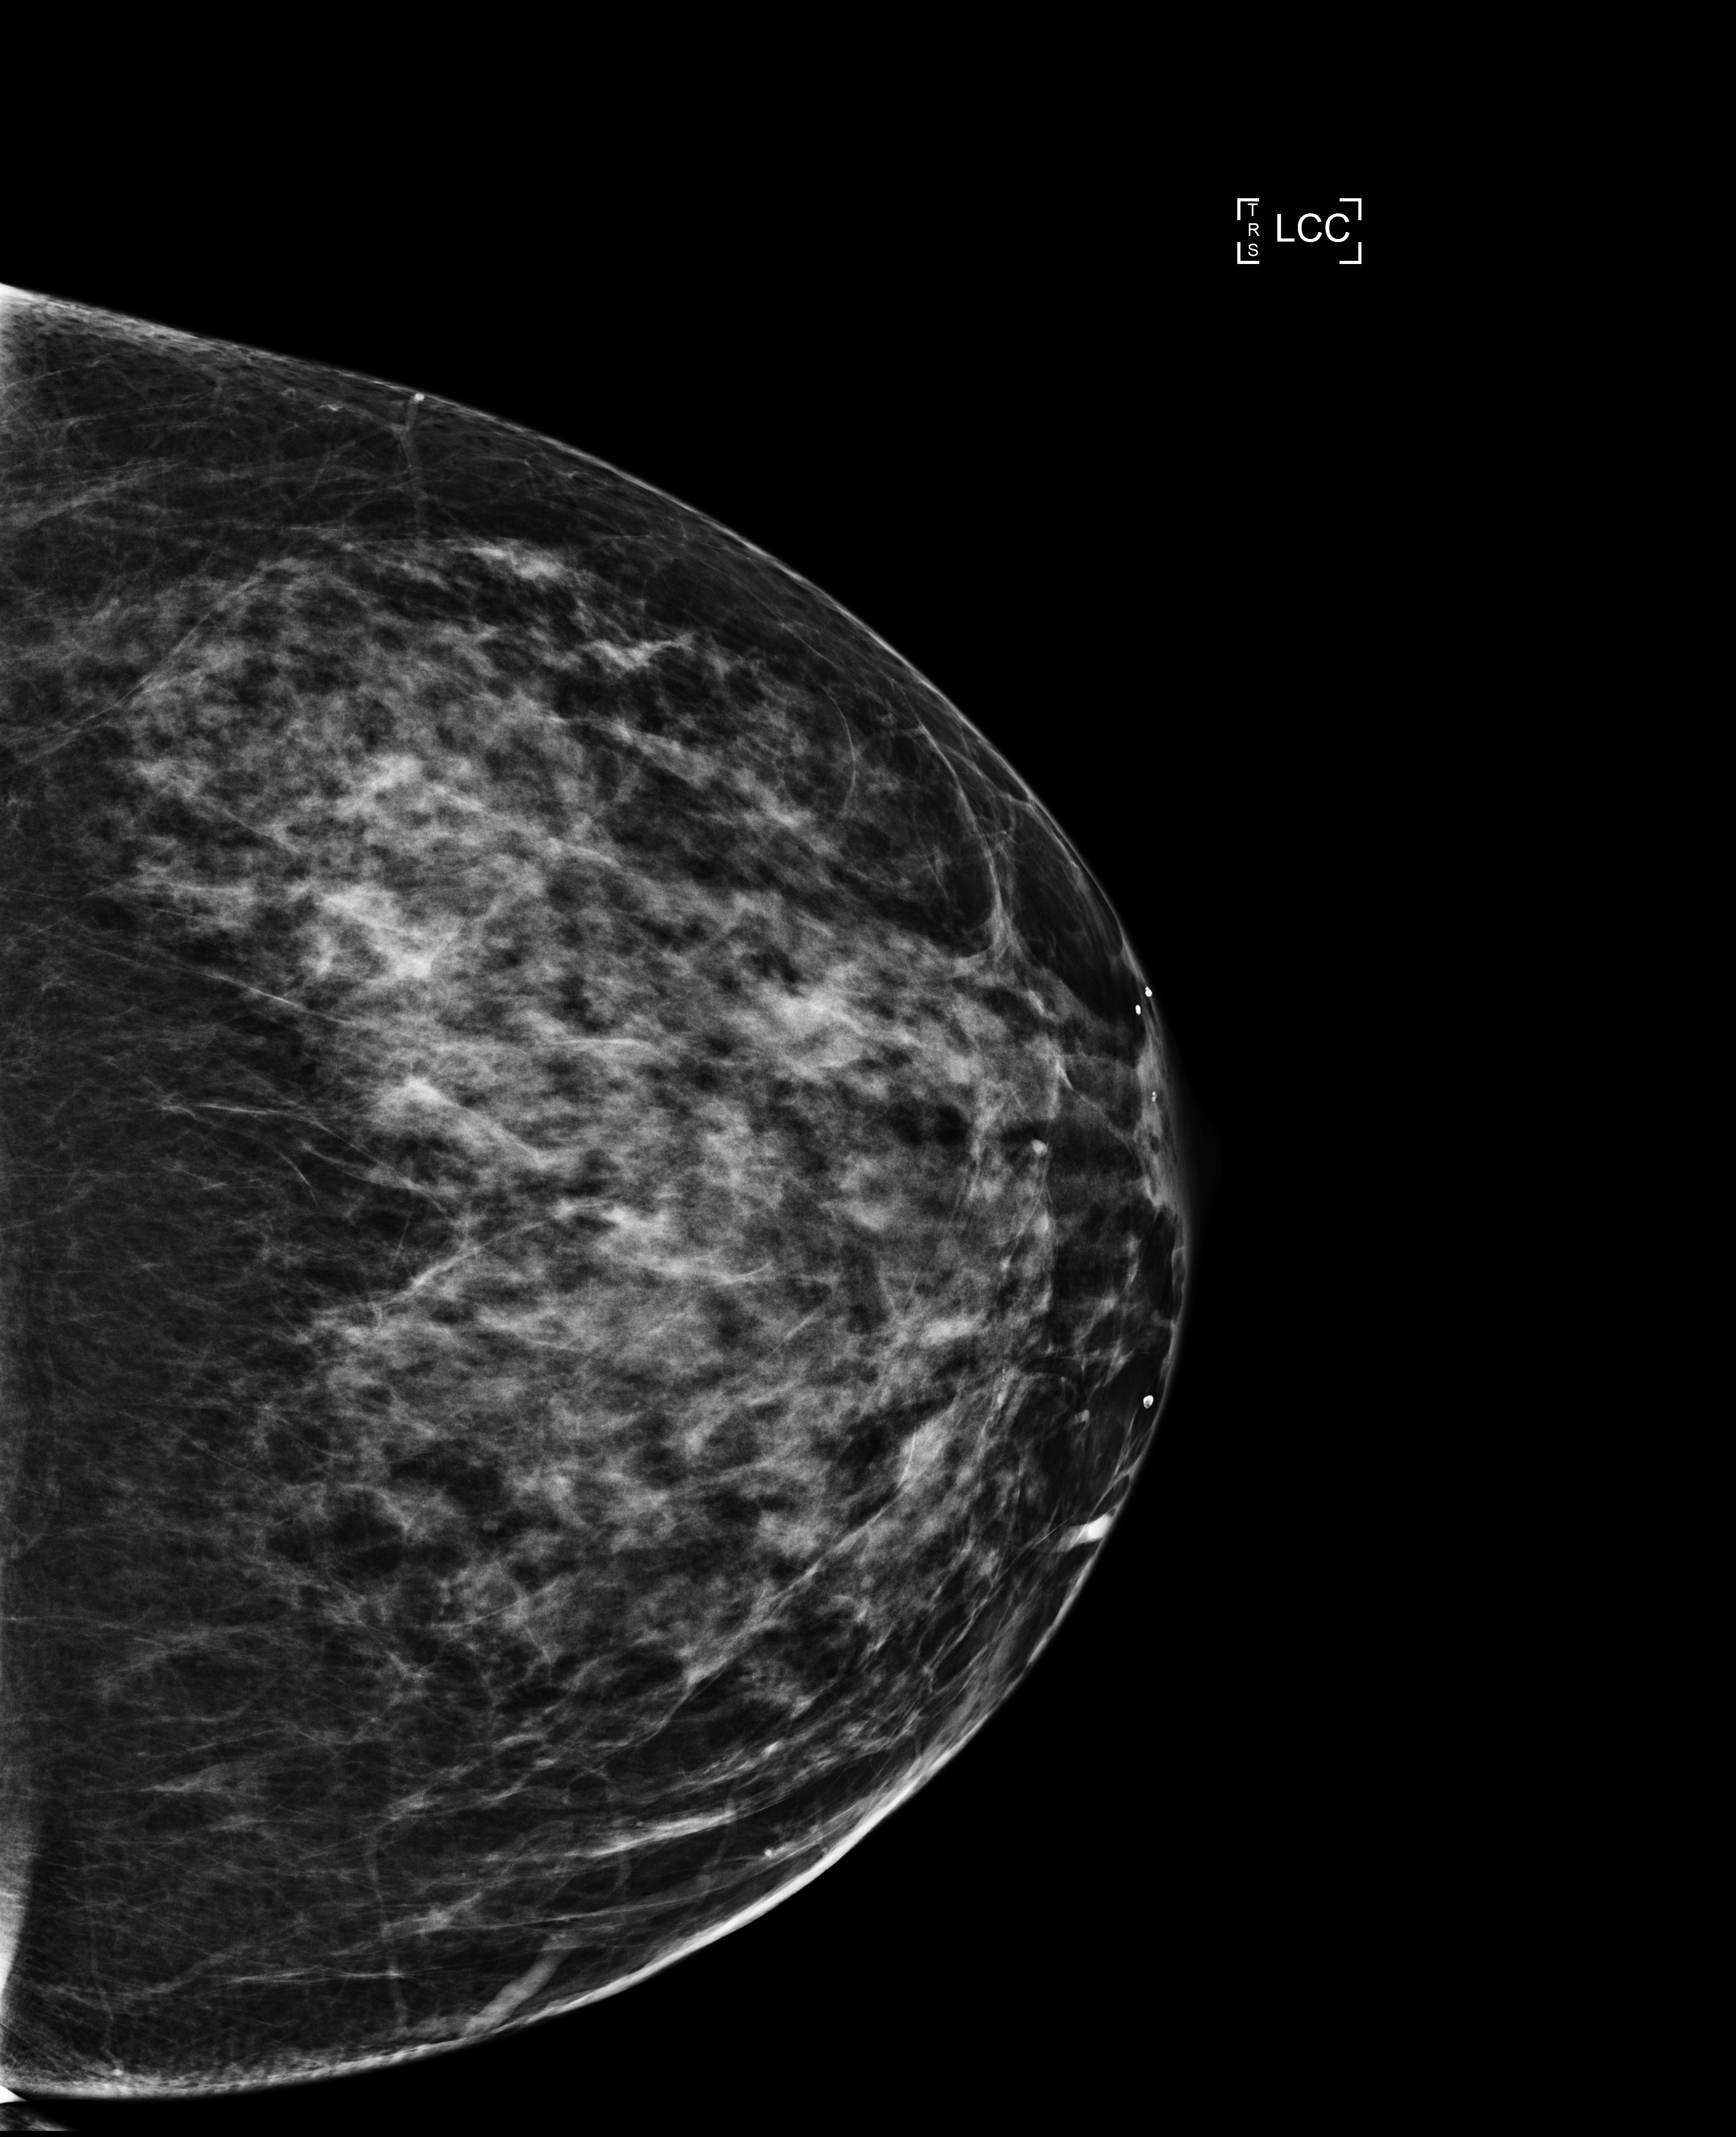
Annual screening mammography examination; compressed breast thickness 76 mm. Patient aged 45 years (female).
Image type: full-field digital mammogram. Breast: left. Projection: CC view.